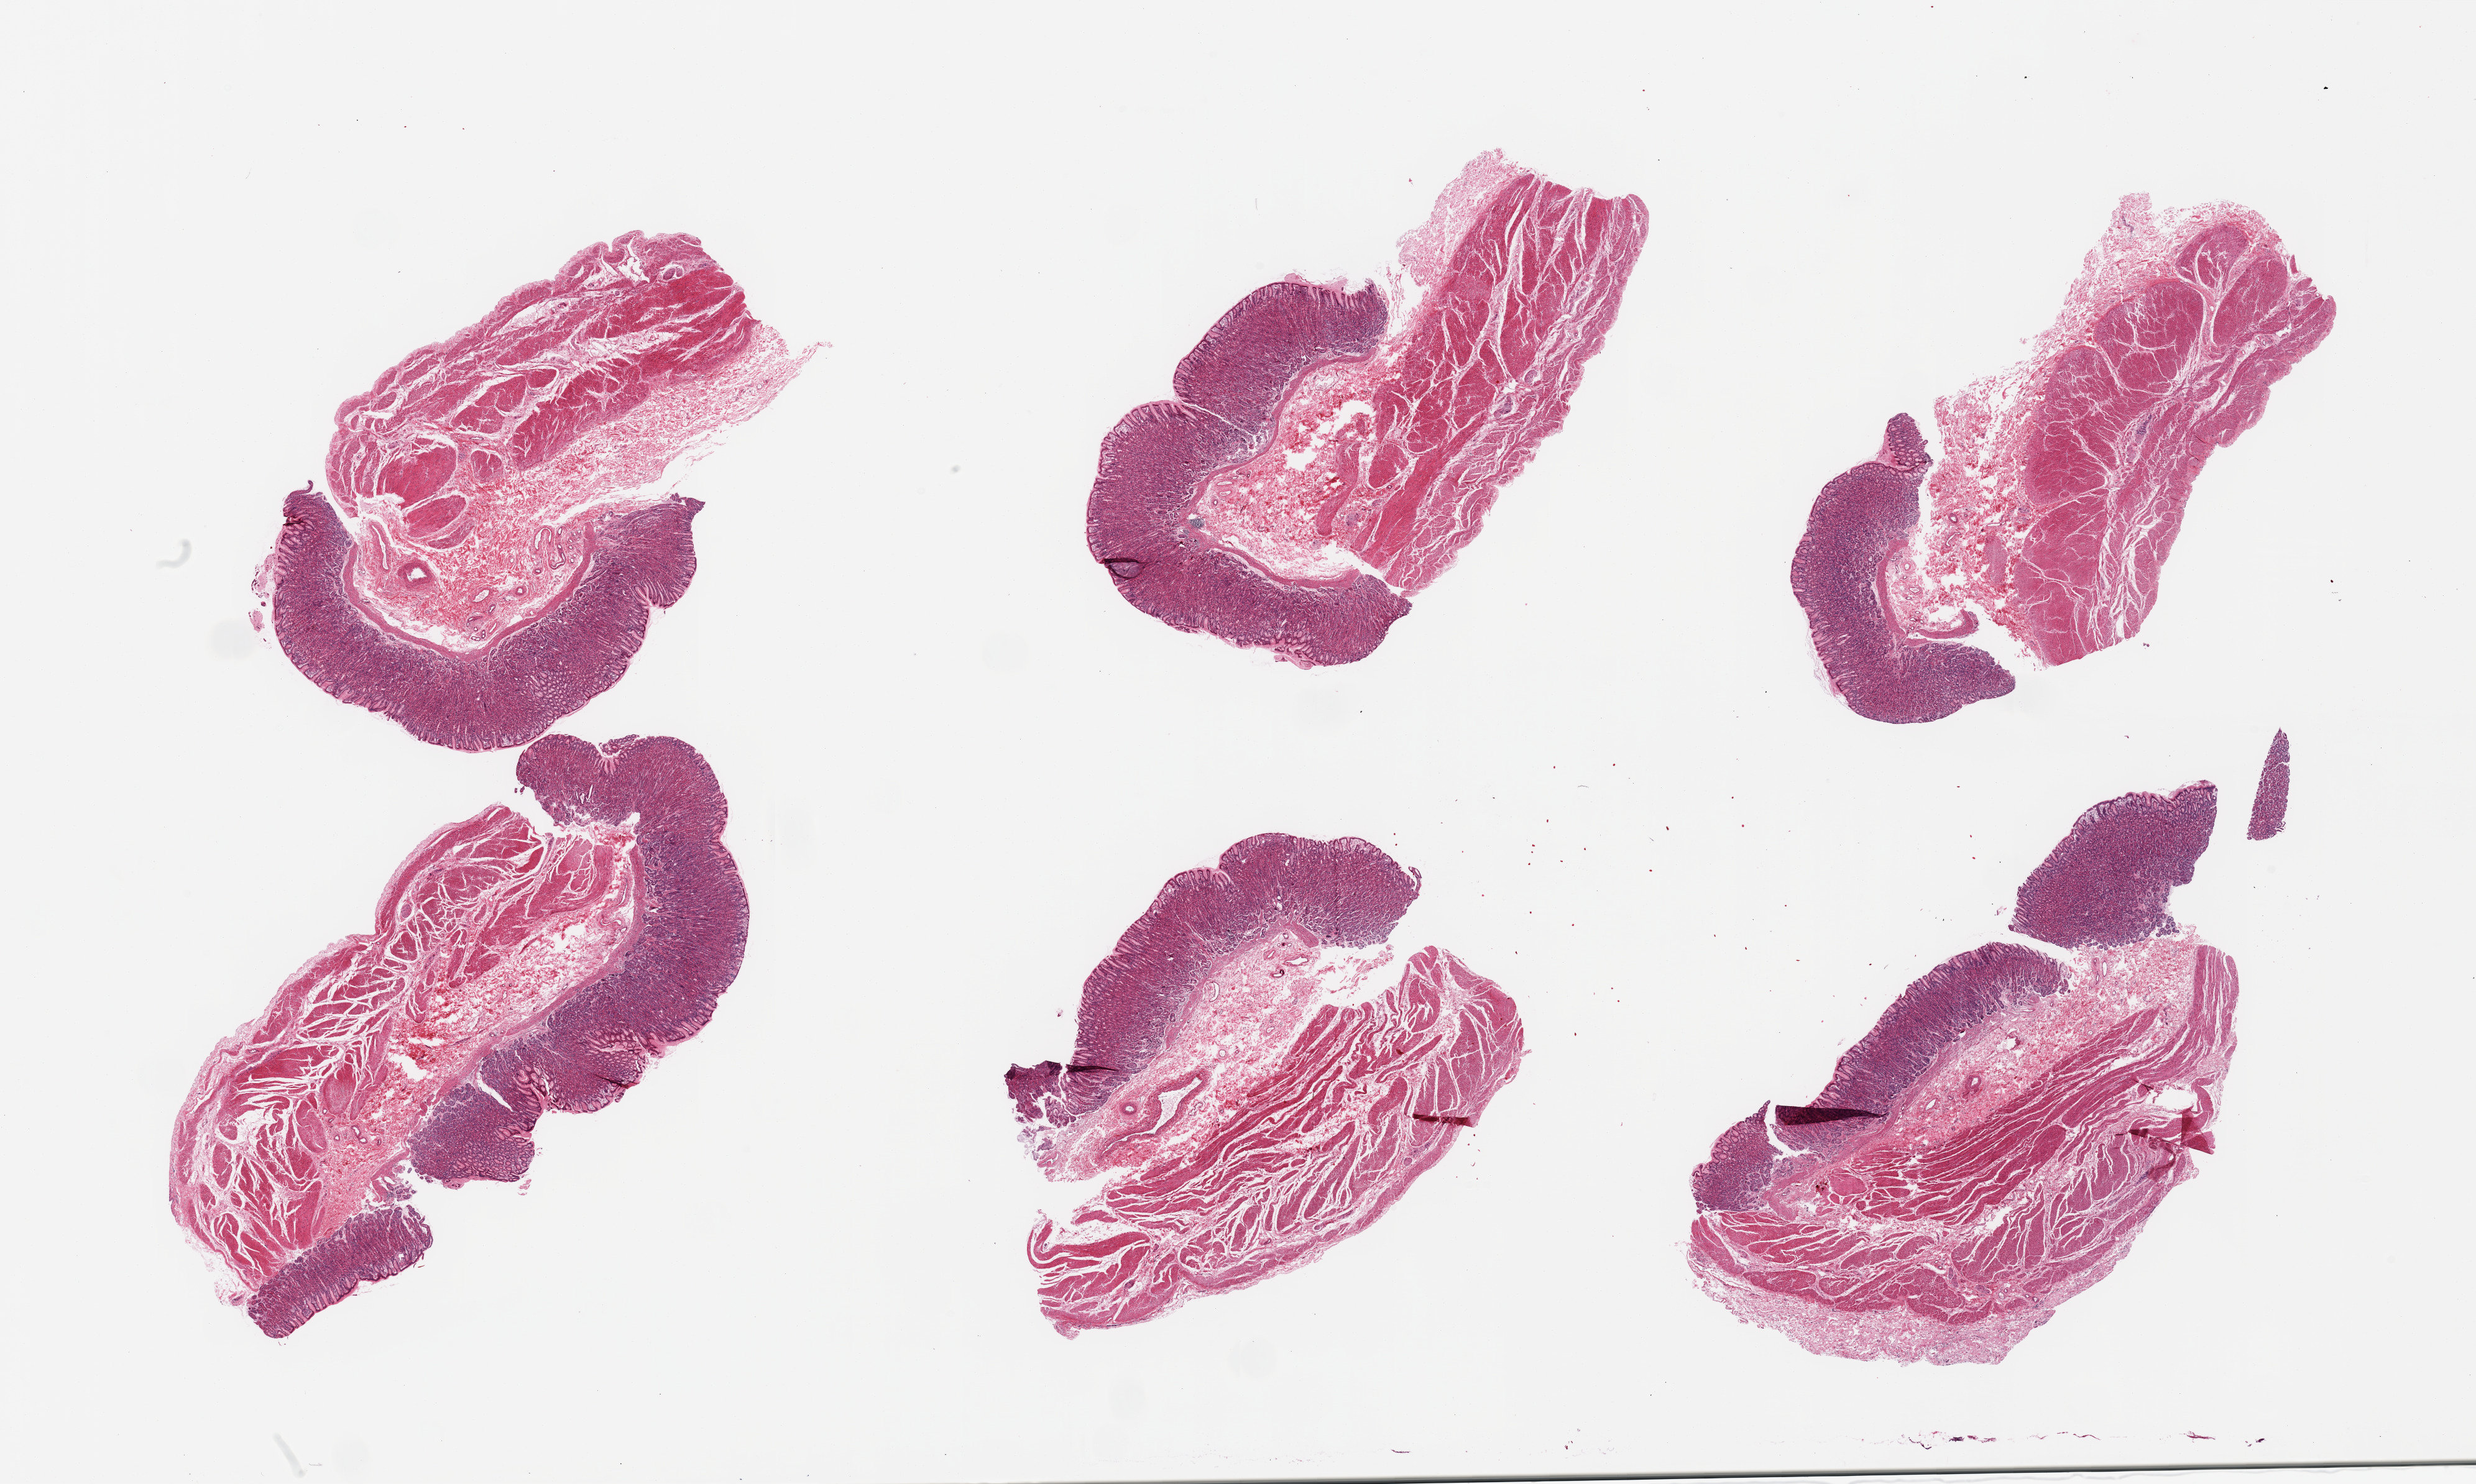
Haematoxylin and eosin whole-slide image, whole scanned area (about 31.5 x 18.9 mm) shown as a low-resolution overview; PAXgene-fixed, paraffin-embedded tissue; sampled site (target tissue): stomach; tissue donor sample.
• review note (as recorded): 6 pieces, mucosa well preserved, up to~ 1mm, ~25% of thickness